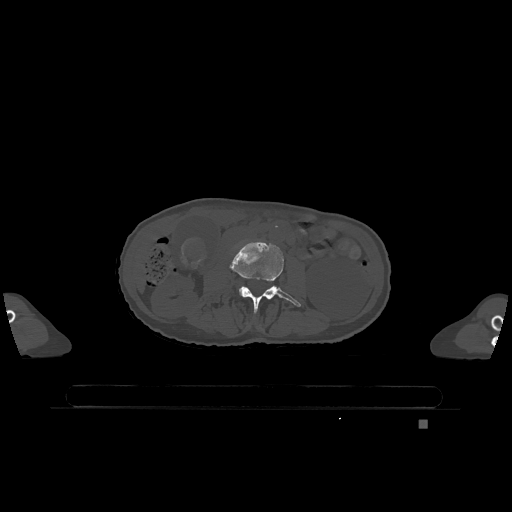
CT including the spine, one axial slice. Position 353 of 1317 along the scan axis. Bone window (W 1800 / L 400 HU). 0.5 mm slice thickness. 512 × 512 image matrix. Female patient, age 74 years. From the clinical record (not read from this slice): primary cancer: lung; vertebrae with lytic lesions (as recorded): T1, T4, T5, T6, L4, L5.
Annotated regions visible in this slice (semi-automatic segmentation, software-assisted and operator-edited):
- L3 vertebra: bounding box [x1, y1, x2, y2] px = [230, 242, 301, 313]